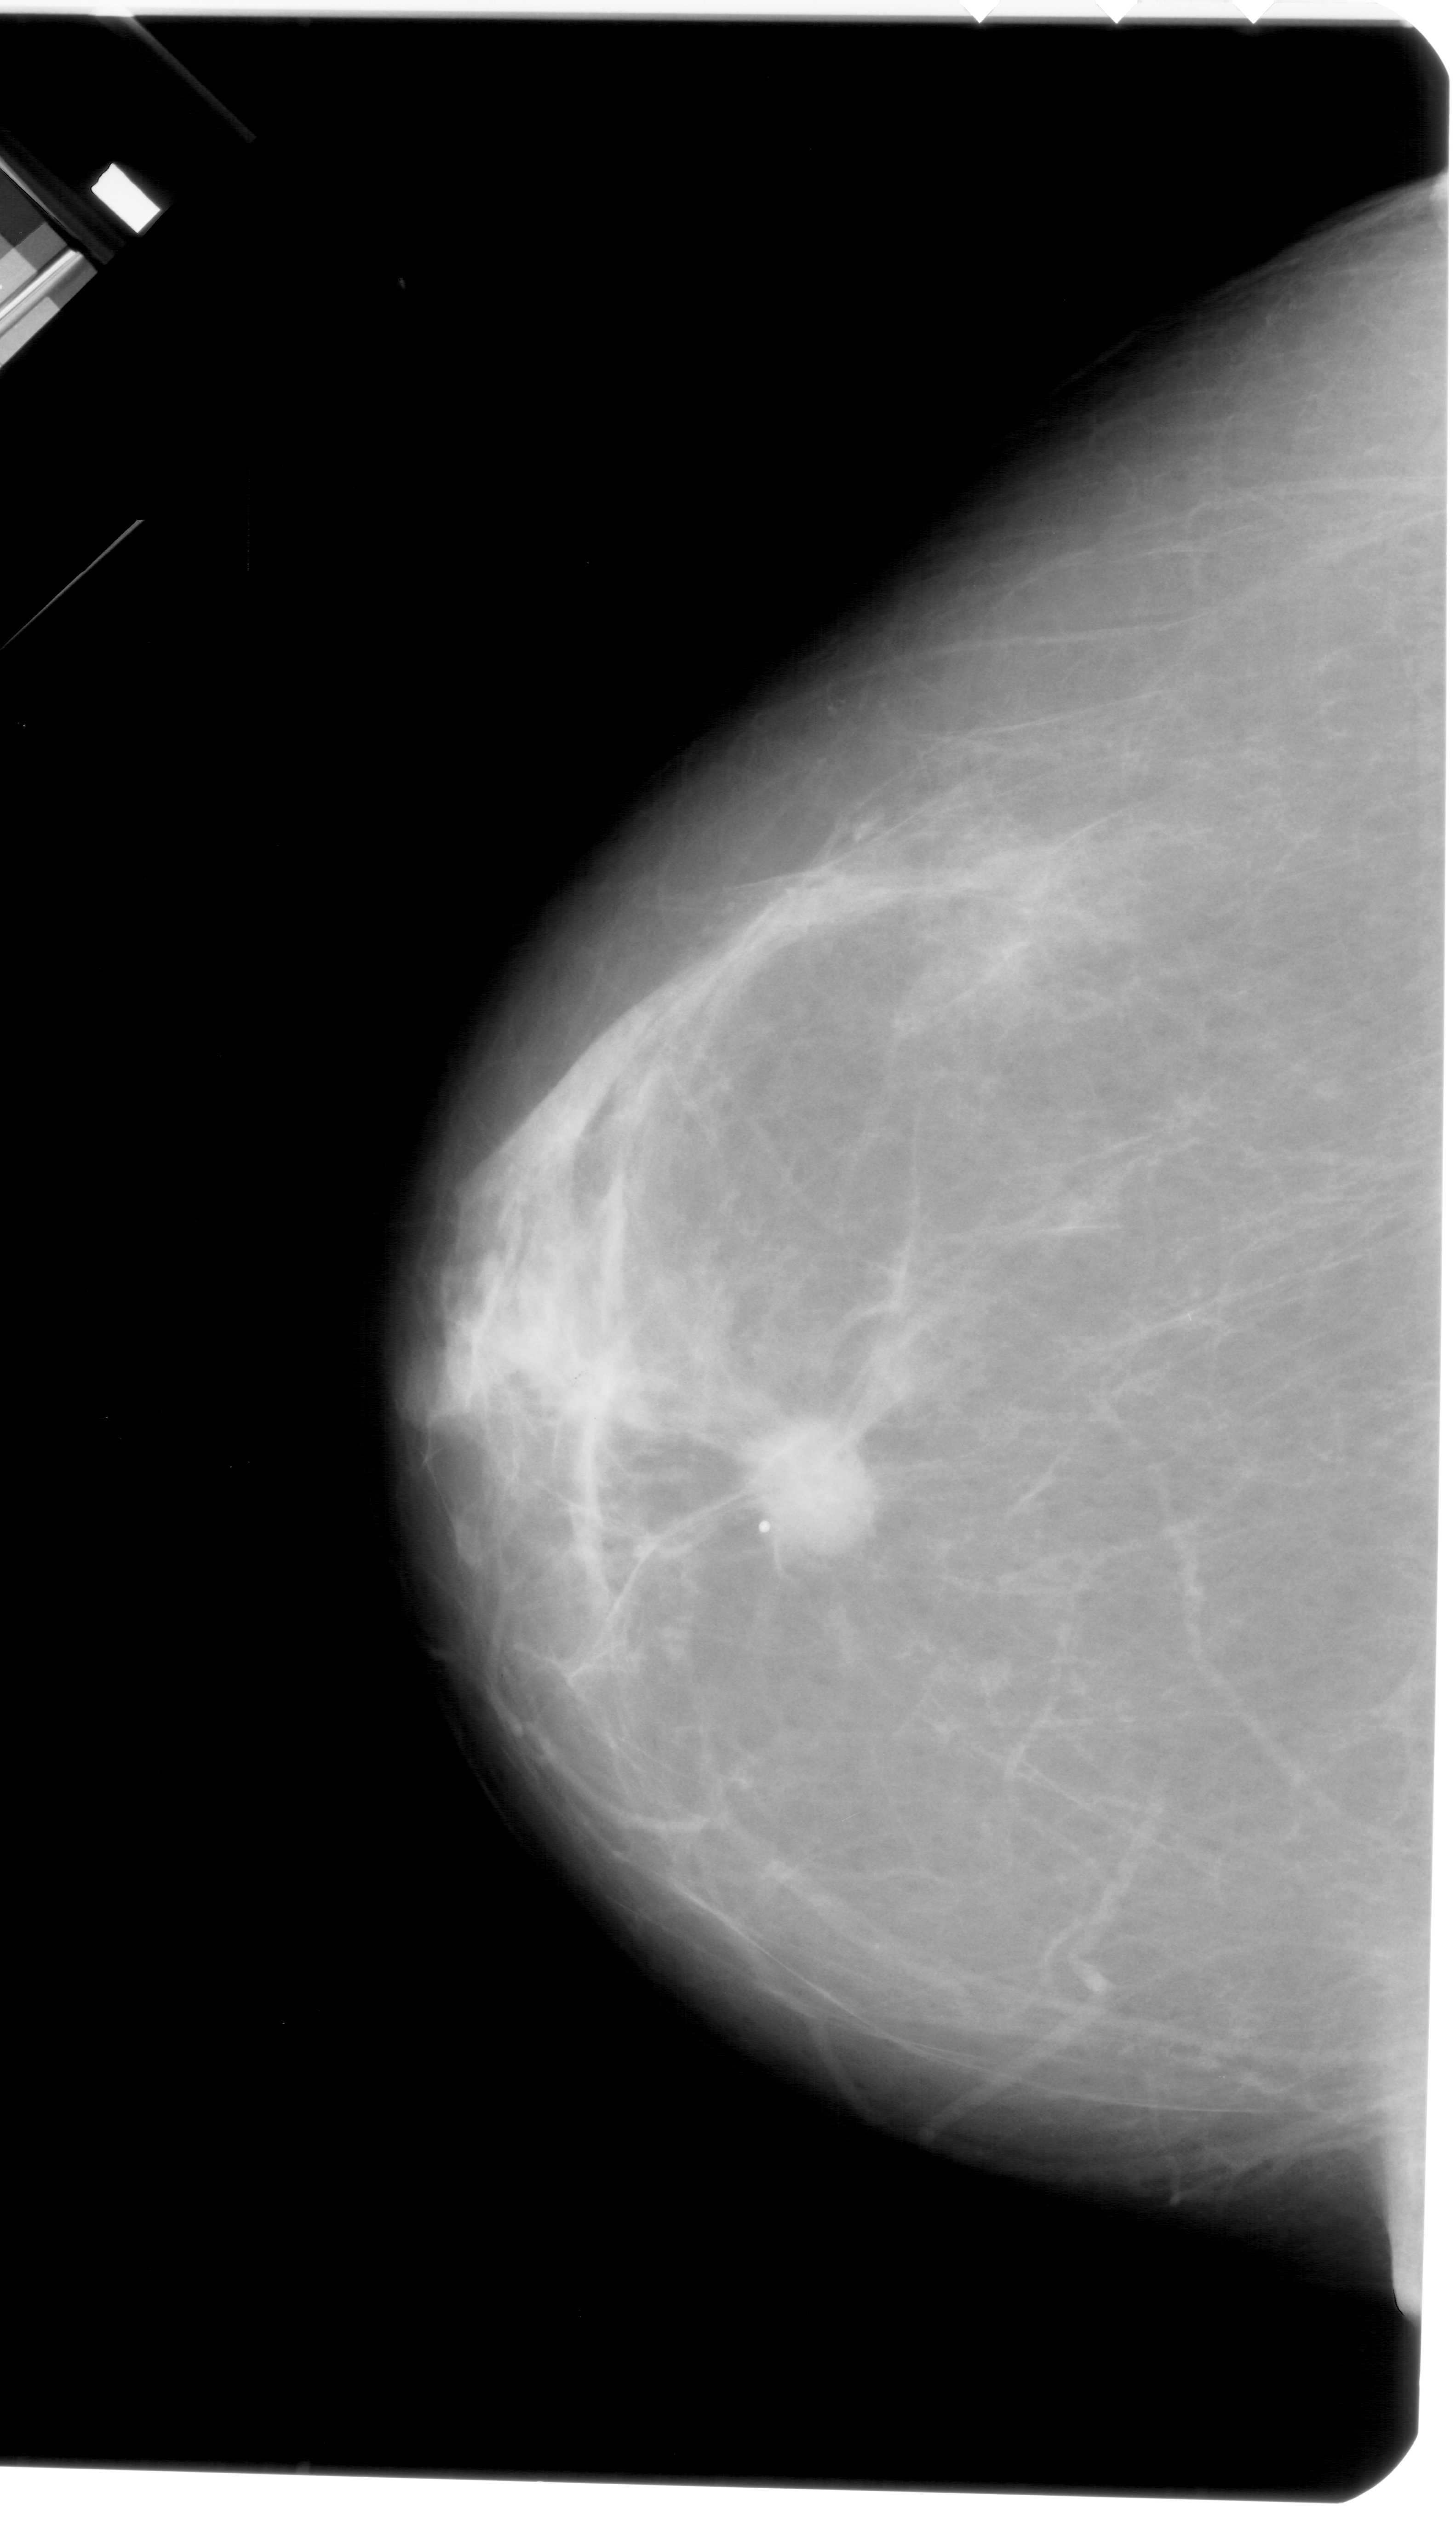
Scanned film-screen mammogram. Left breast. Craniocaudal (CC) view. BI-RADS breast density category 1 (scale 1–4). 1456 × 2526 image matrix.
Expert-marked regions of interest on this film, with their recorded descriptors:
- mass, shape oval, margins spiculated; BI-RADS assessment category 5; pathology (as recorded): malignant: box from (x=644, y=1338) to (x=973, y=1599) px